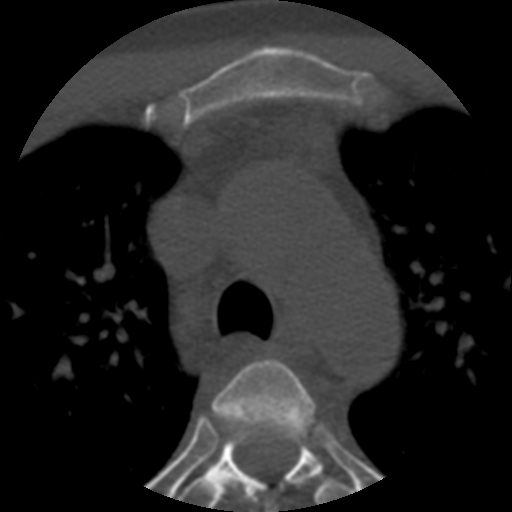
CT including the spine, one axial slice; position 404 of 508 along the scan axis; bone window (W 1800 / L 400 HU); 1.25 mm slice thickness; 512 × 512 image matrix, field of view 160 × 160 mm. Patient age 57 years. Case-level facts recorded for this patient, not image findings: primary cancer: prostate.
Outlined on this slice (semi-automatic segmentation, software-assisted and operator-edited):
- T3 vertebra: bounding box (x1, y1, x2, y2) in pixels: (212, 359, 315, 512)
- T4 vertebra: (178, 422, 361, 512)